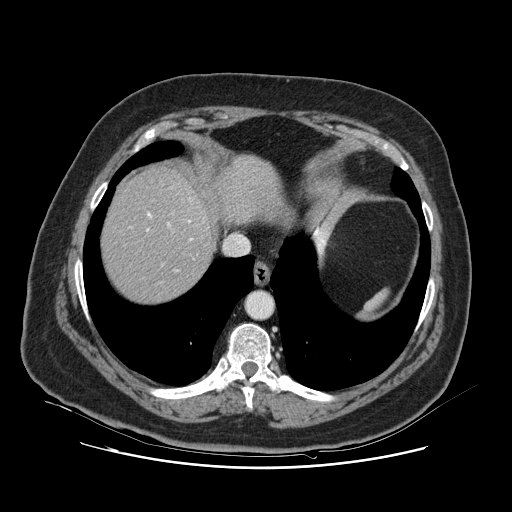
Contrast-enhanced abdominal CT, one axial slice. Slice 106 of 132 in the series (ordered by position). 120 kVp. Intravenous contrast given. Soft-tissue window (W 400 / L 40 HU). 2.5 mm slice thickness. 512 × 512 image matrix. Female patient, age 73 years. Case-level facts recorded for this patient, not image findings: diagnosis: colorectal cancer liver metastases, imaged before liver resection; multiple liver metastases: no; largest metastasis: 7 cm.
Annotated regions visible in this slice (expert manual segmentation):
- hepatic veins: bounding box (x1, y1, x2, y2) in pixels: (131, 213, 193, 272)
- liver: (103, 170, 294, 302)
- planned liver remnant (the part of the liver to remain after resection): (103, 170, 213, 303)
- portal vein (with intrahepatic branches): (168, 224, 170, 227)